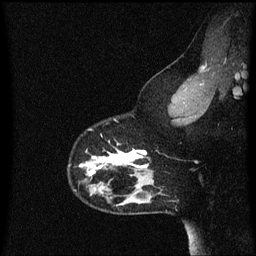
Breast MRI (dynamic contrast-enhanced), one sagittal slice; slice 48 of 60 in the series (ordered by position); dynamic contrast-enhanced series, image 2 of 3 at this slice position (ordered by acquisition); 1.5 T; TE 4.2 ms, TR 8.4 ms; 2 mm slice thickness; 256 × 256 image matrix, field of view 200 × 200 mm. Patient: female, 33 years.
Structures marked on this image (semi-automatic segmentation, software-assisted and operator-edited):
- analysis volume of interest (the breast-tissue region the enhancement analysis was run in; not a lesion): bounding box [x1, y1, x2, y2] px = [69, 118, 152, 191]
- tumour enhancement mask (voxels above the 70 % enhancement threshold inside the analysis volume of interest): [80, 144, 149, 177]